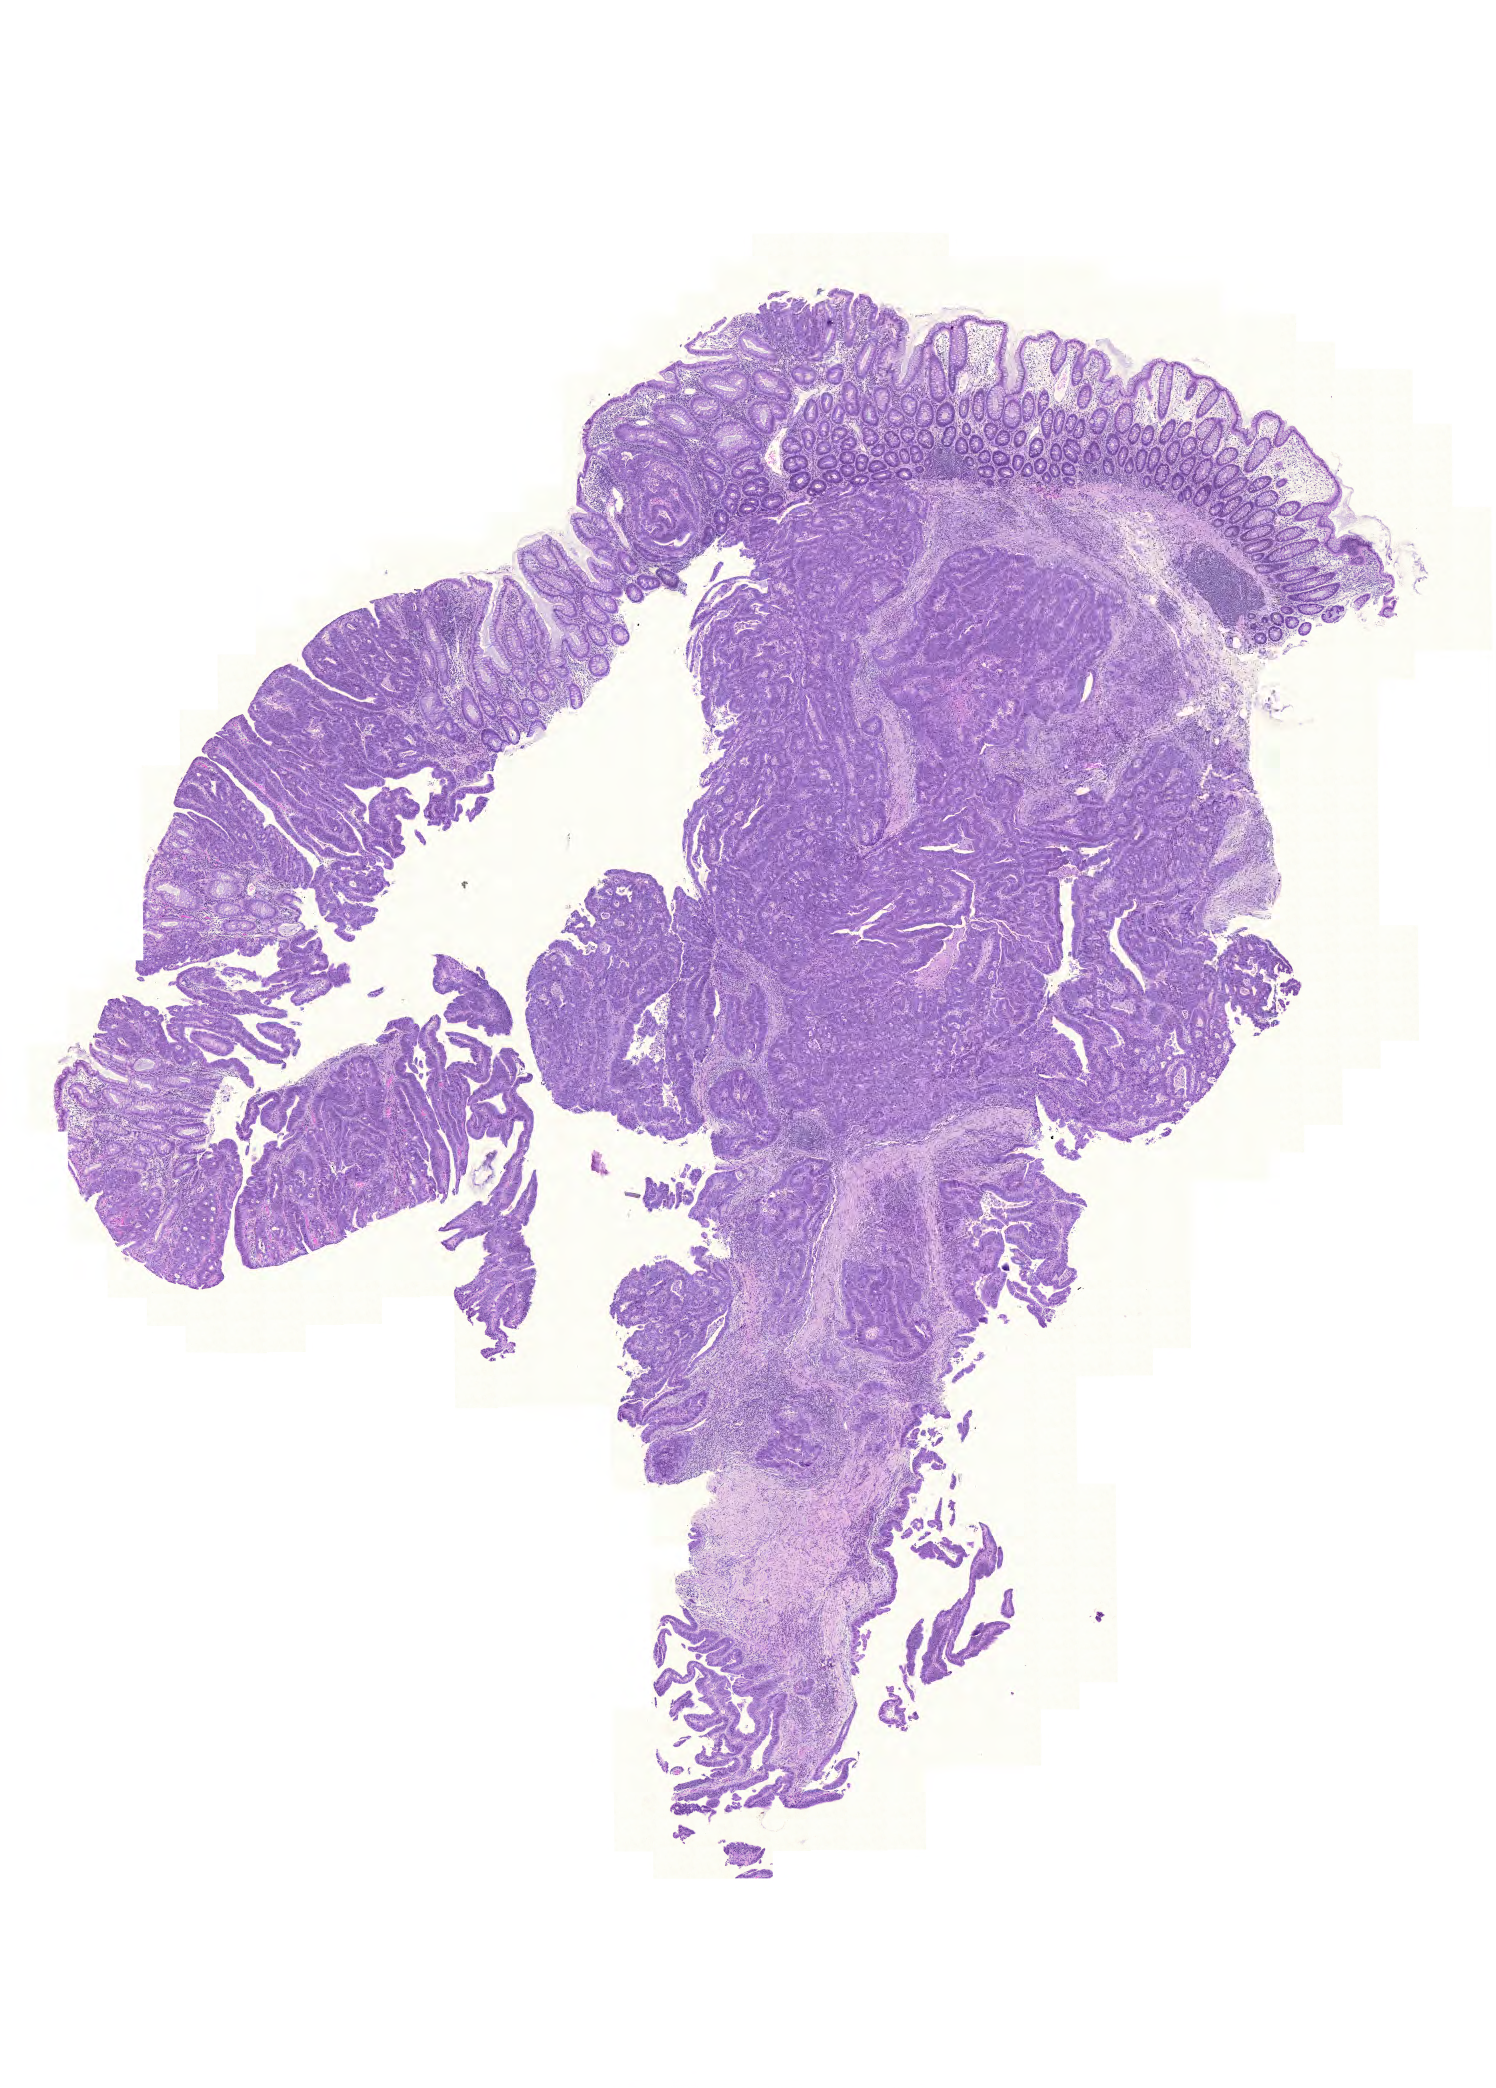
H&E-stained whole-slide image — low-resolution overview of the scanned area, about 11.1 x 15.5 mm (from a 20x scan). Formalin-fixed paraffin-embedded (FFPE) diagnostic section. Primary tumour sample from the rectum. Patient: male, age at initial diagnosis 61 years.
- AJCC pathologic stage: IIA (6th edition)
- diagnosis: Adenocarcinoma, NOS (rectosigmoid junction)
- lymph nodes positive (case pathology): 0 of 17 examined